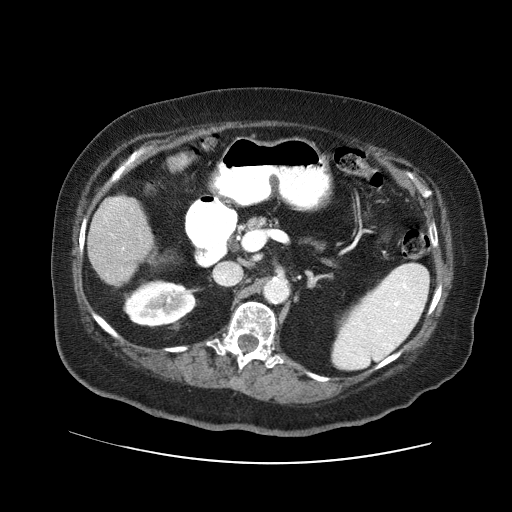
Contrast-enhanced abdominal CT (liver protocol), one axial slice; slice 17 of 71 in the series (ordered by position); 120 kVp; soft-tissue window (W 400 / L 40 HU); 512 × 512 image matrix. Case-level facts recorded for this patient, not image findings: diagnosis: hepatocellular carcinoma (patient treated with transarterial chemoembolisation; whether this scan precedes or follows treatment is not stated here); TNM stage (as recorded): Stage-II; Child-Pugh class: A; tumour differentiation: poorly differentiated; tumour nodularity: multinodular.
Structures marked on this image (semi-automatic segmentation, software-assisted and operator-edited):
- liver parenchyma outside the tumour (the mass and vessels are separate outlines, so this box may not span the whole liver): bounding box [x1, y1, x2, y2] px = [88, 154, 190, 286]
- liver vessels: [116, 199, 124, 249]